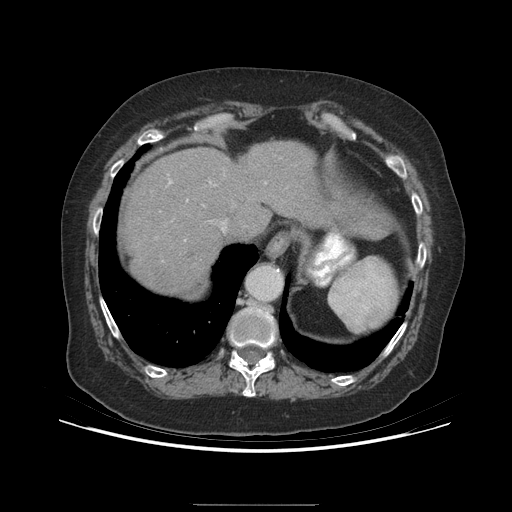
Contrast-enhanced abdominal CT (liver protocol), one axial slice. Position 175 of 192 along the scan axis. Reconstruction kernel STANDARD. 140 kVp. Soft-tissue window (W 400 / L 40 HU). 512 × 512 image matrix. Case-level facts recorded for this patient, not image findings: diagnosis: hepatocellular carcinoma (patient treated with transarterial chemoembolisation; whether this scan precedes or follows treatment is not stated here); TNM stage (as recorded): Stage-I; Child-Pugh class: A; tumour differentiation: moderately differentiated; tumour nodularity: uninodular.
Structures marked on this image (semi-automatic segmentation, software-assisted and operator-edited):
- liver parenchyma outside the tumour (the mass and vessels are separate outlines, so this box may not span the whole liver): bounding box (x1, y1, x2, y2) in pixels: (124, 142, 370, 292)